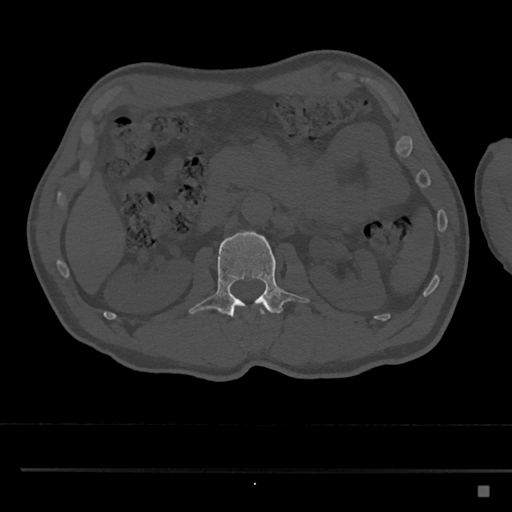
CT including the spine, one axial slice. Position 770 of 797 along the scan axis. 120 kVp. Bone window (W 1800 / L 400 HU). 0.5 mm slice thickness. 512 × 512 image matrix. Patient: male, 59 years. Case-level facts recorded for this patient, not image findings: primary cancer: prostate.
Structures marked on this image (semi-automatically segmented with operator editing):
- L1 vertebra: box from (x=262, y=311) to (x=264, y=313) px
- L2 vertebra: (x=189, y=231)–(x=310, y=321)